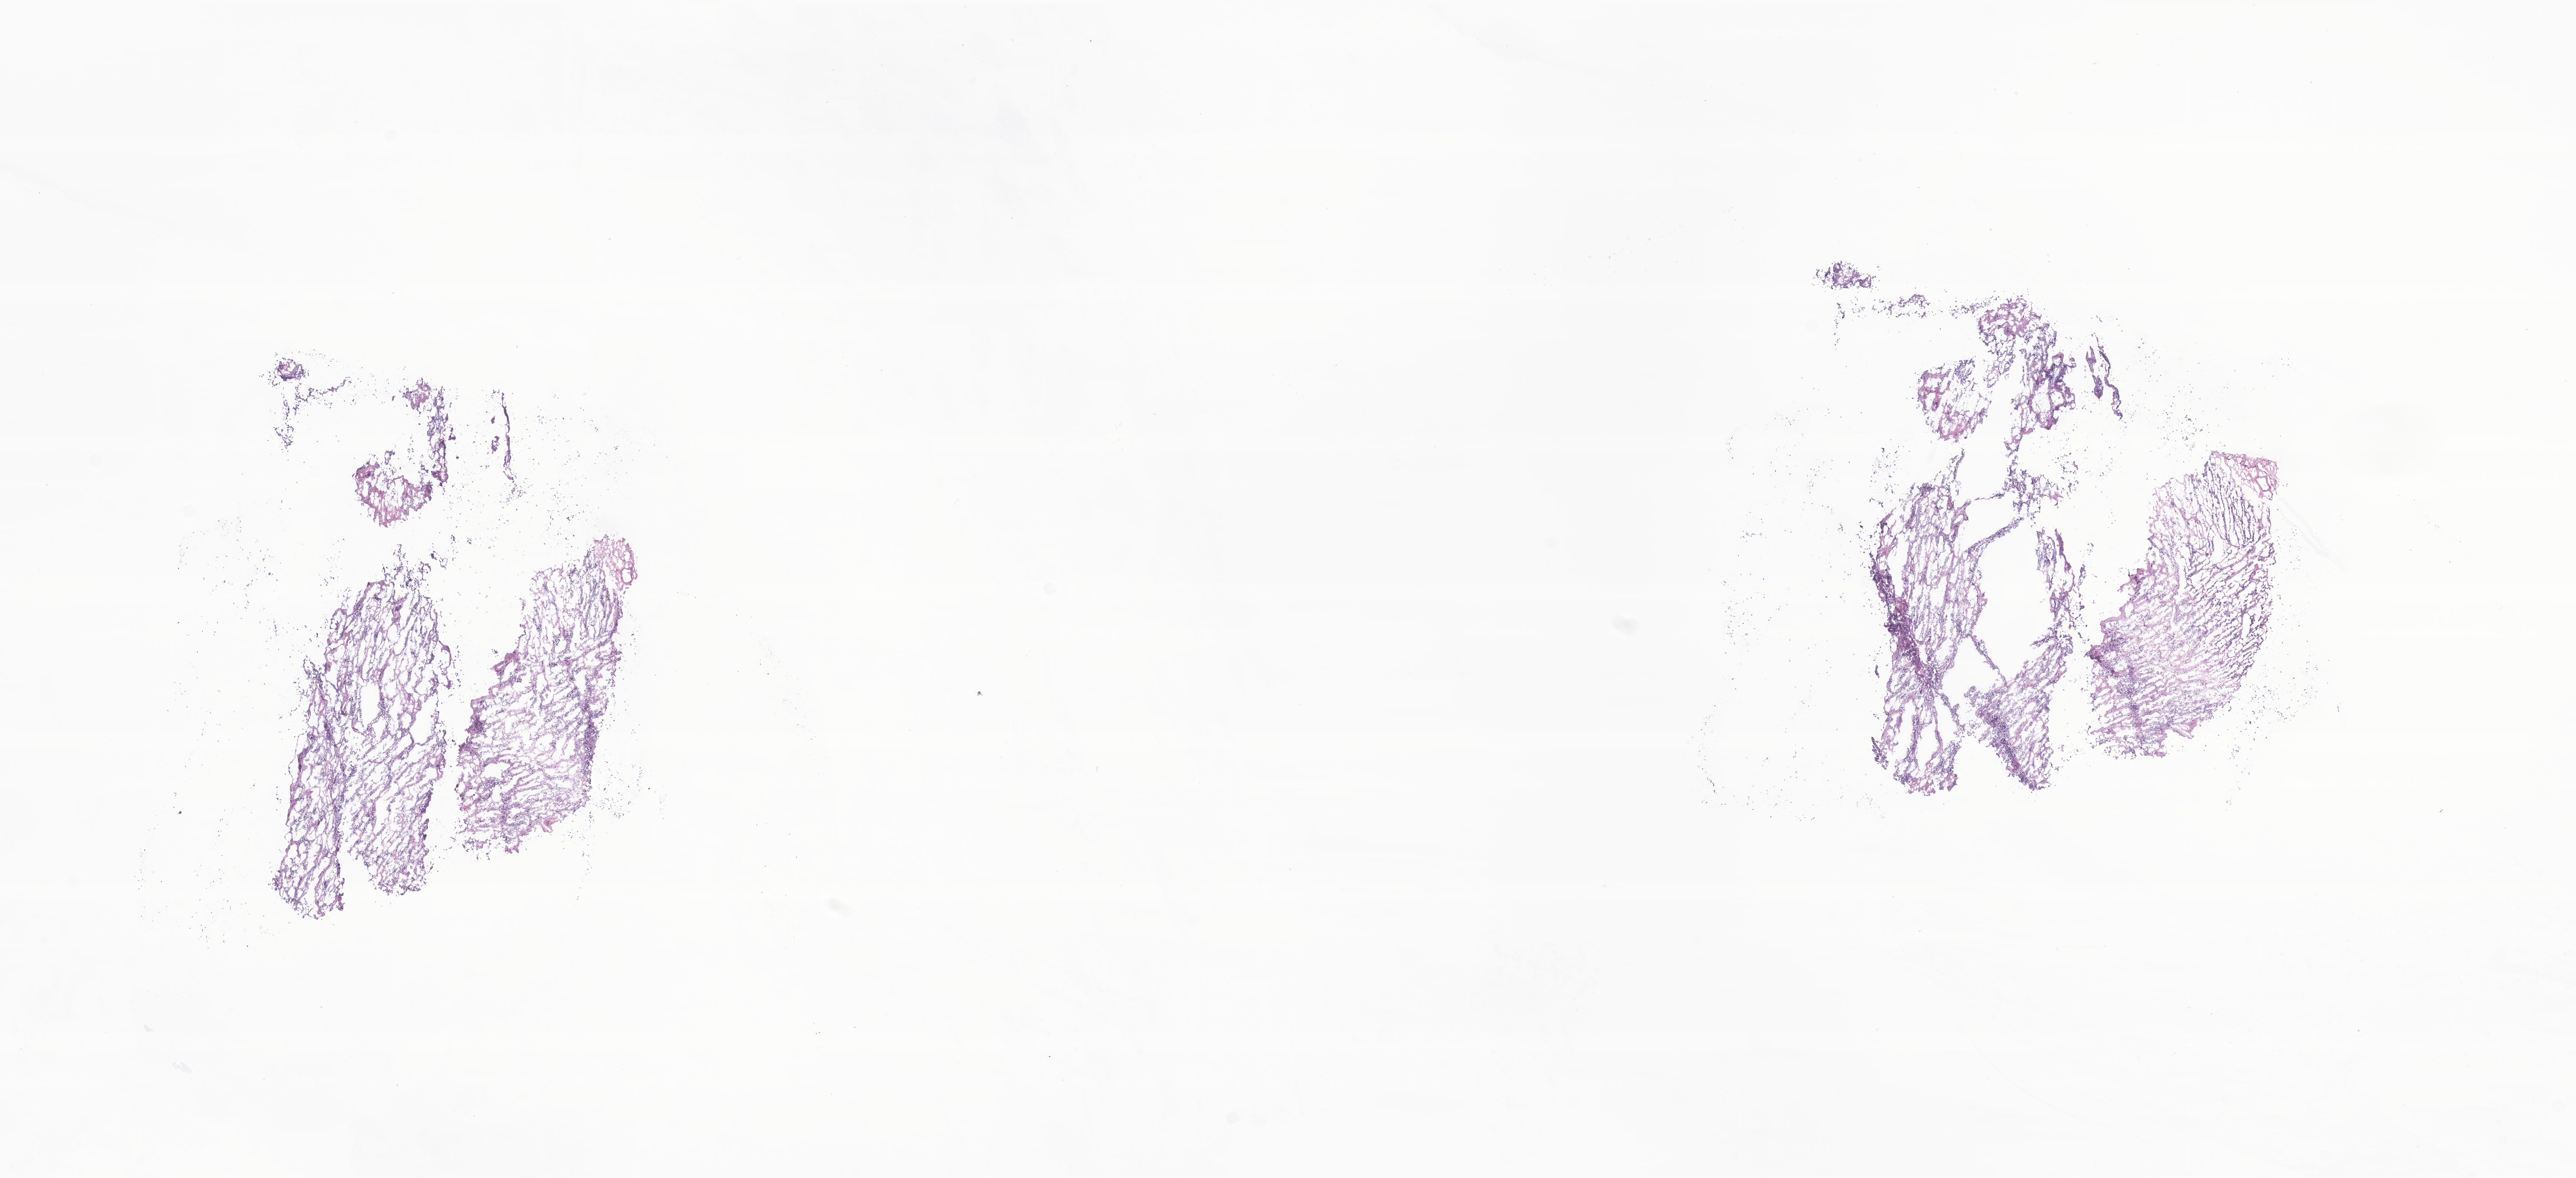
Digitized hematoxylin and eosin (H&E)-stained section of tumor tissue from the abdomen — low-resolution overview of the scanned area, about 18.4 x 8.4 mm. Cryosection (OCT / tissue freezing medium). Patient: female, age 943 days (about 2.6 years).
* diagnosis (ICD-O-3 morphology term): Neuroblastoma, NOS